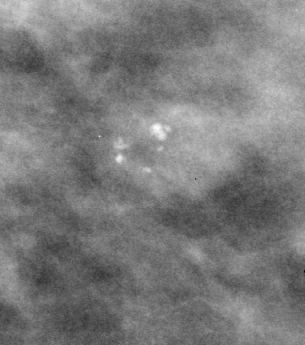
Crop from a digitized film mammogram around one marked abnormality, left breast, MLO view, BI-RADS breast density category 2 (scale 1–4).
Marked abnormality: calcifications, morphology punctate, distribution clustered; BI-RADS assessment category 3; pathology result (as recorded, not read from the image): benign.